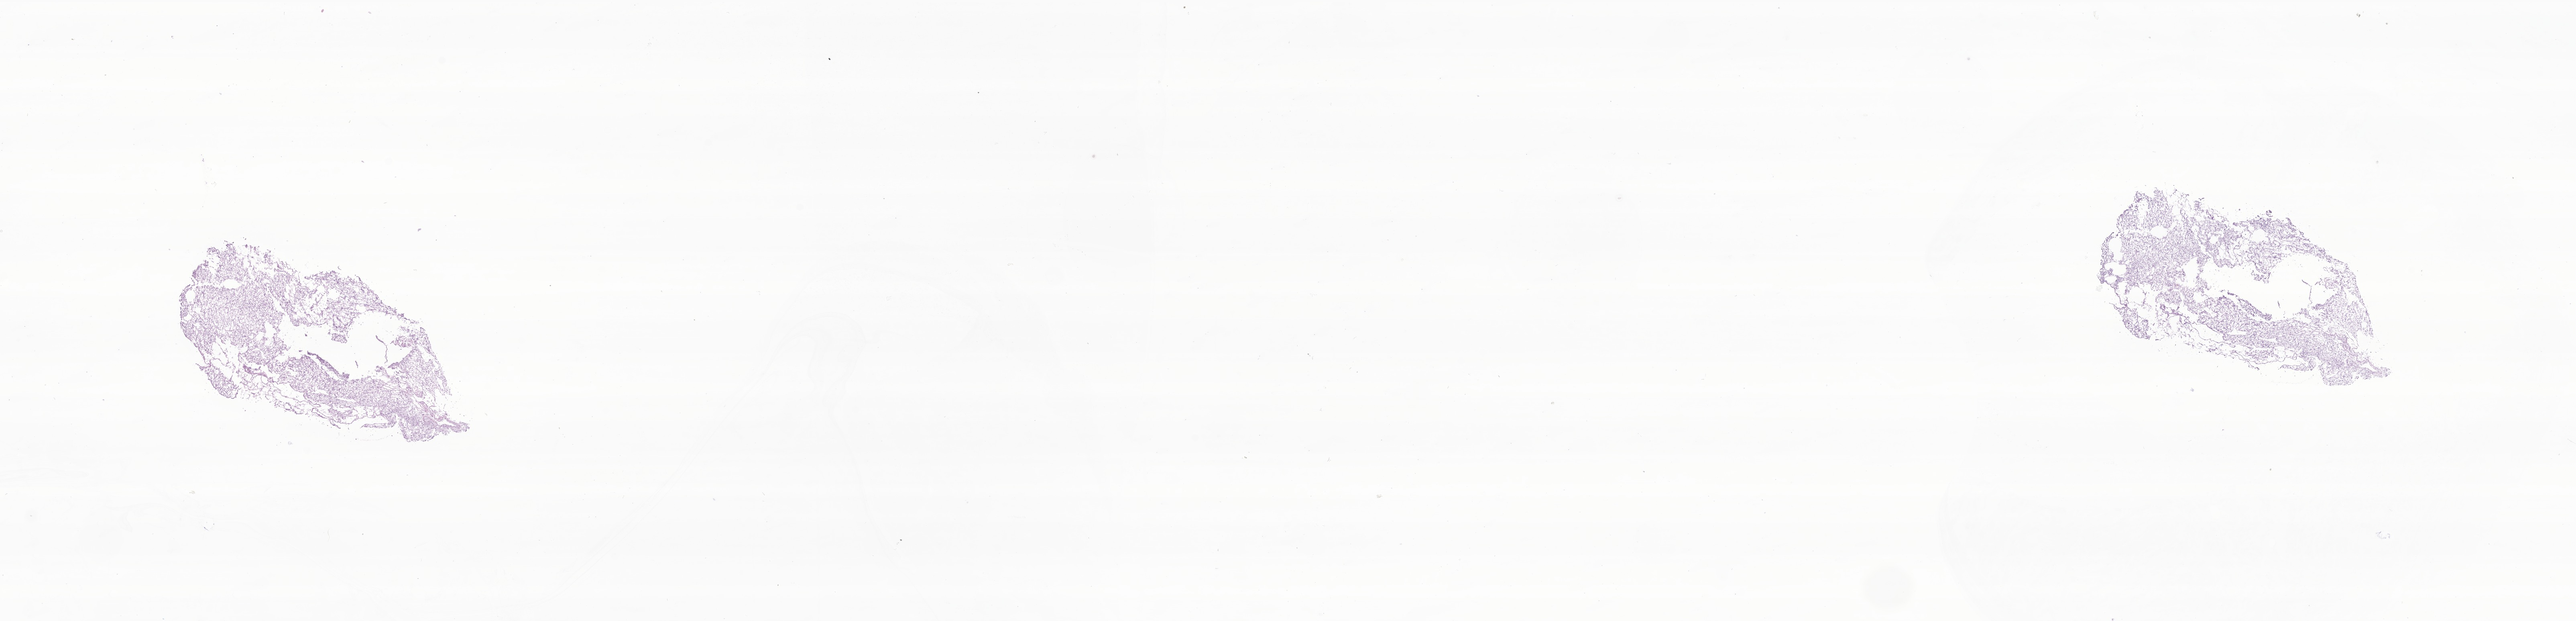
Haematoxylin and eosin whole-slide image of tumor tissue from the brain — shown as a low-resolution overview of the whole scanned area (about 26.9 x 6.5 mm), cryosection (OCT / tissue freezing medium). Patient: male, age 208 months (17 years 4 months).
Diagnosis (ICD-O-3 morphology term): Neoplasm, uncertain whether benign or malignant.